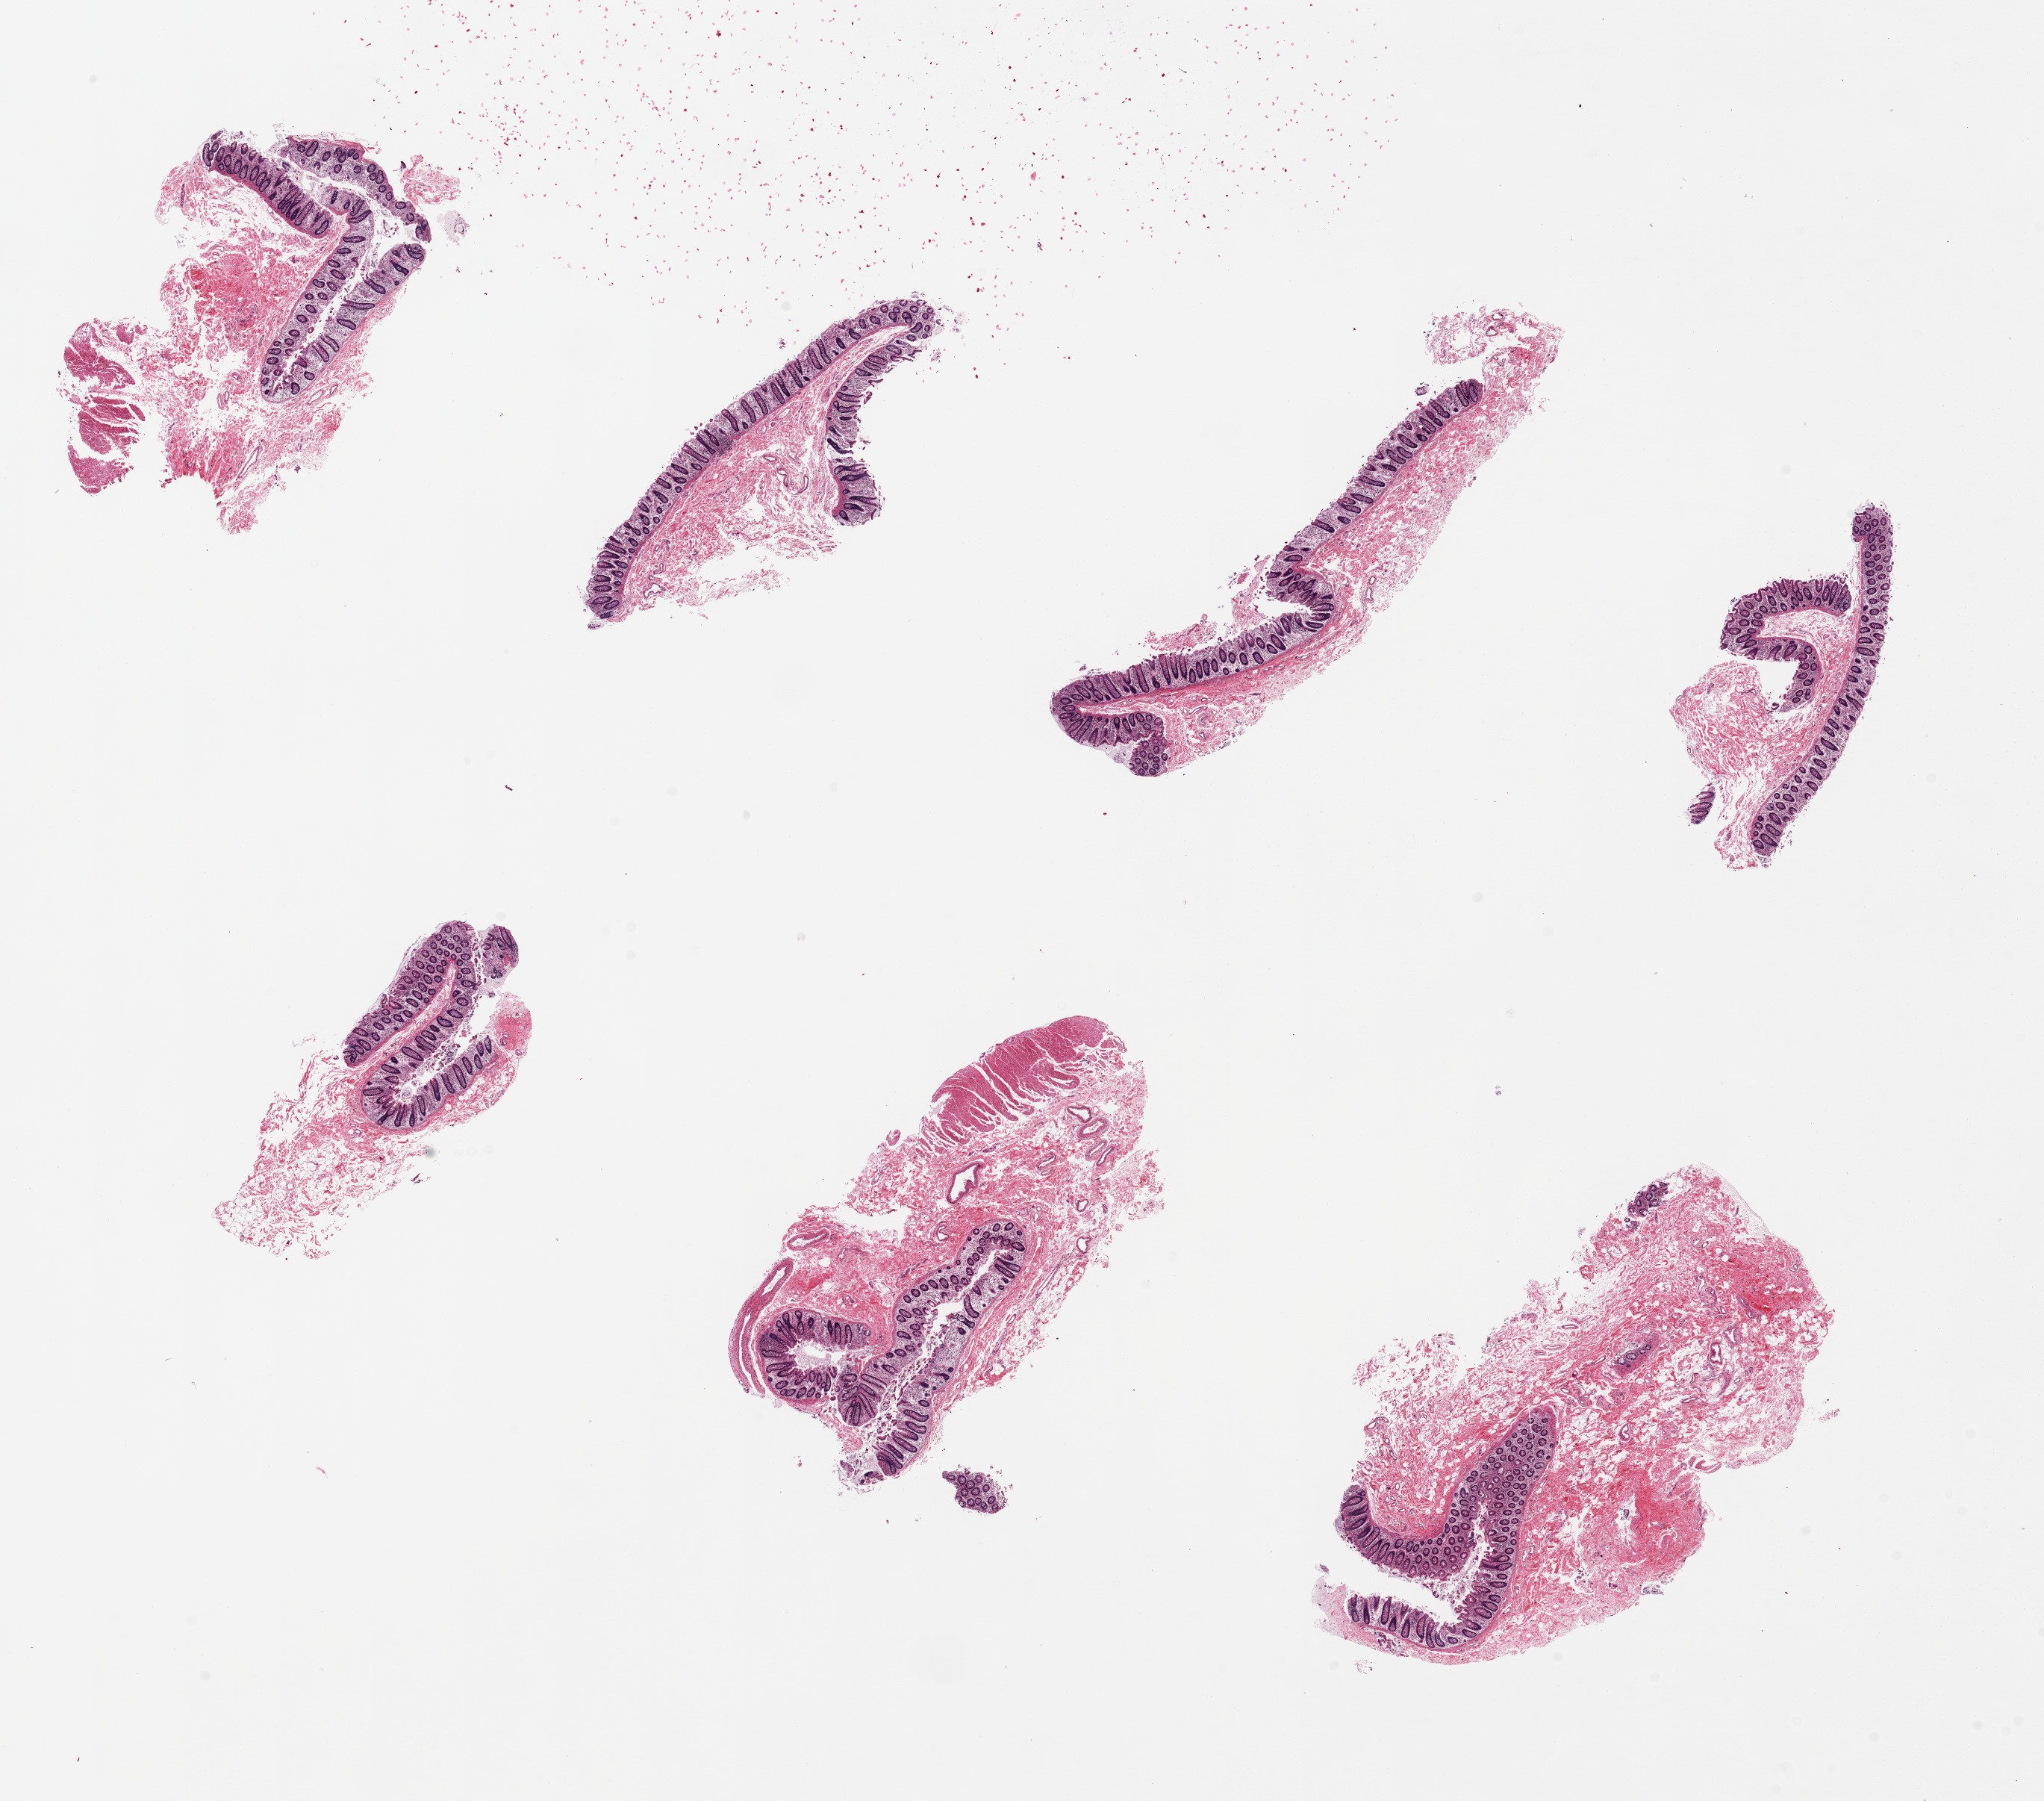
Digitized hematoxylin and eosin (H&E)-stained section, brightfield — shown as a low-resolution overview of the whole scanned area (about 21.7 x 19.1 mm, from a 20x scan). PAXgene-fixed, paraffin-embedded tissue. Sampled site (target tissue): ileum. Donor tissue sample. Donor sex: female.
Review note (as recorded): 7 pieces, up to 7x2mm; 10% mucosa, all colonic, not ileal origin; may be used as colon when corrected.